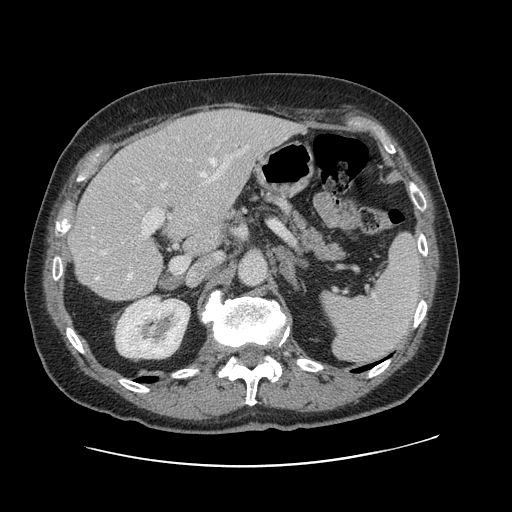
Contrast-enhanced abdominal CT, one axial slice. Slice 66 of 138 in the series (ordered by position). 120 kVp. Soft-tissue window (W 400 / L 40 HU). 2.5 mm slice thickness. 512 × 512 image matrix, field of view 402 × 402 mm. Male patient, age 71 years. Case-level facts recorded for this patient, not image findings: diagnosis: colorectal cancer liver metastases, imaged before liver resection; multiple liver metastases: no; largest metastasis: 3.3 cm; disease in both lobes: no.
Structures marked on this image (outlined manually by an expert reader):
- hepatic veins: bounding box (x1, y1, x2, y2) in pixels: (92, 158, 224, 280)
- liver: (71, 109, 297, 300)
- planned liver remnant (the part of the liver to remain after resection): (71, 144, 219, 300)
- portal vein (with intrahepatic branches): (91, 145, 249, 255)